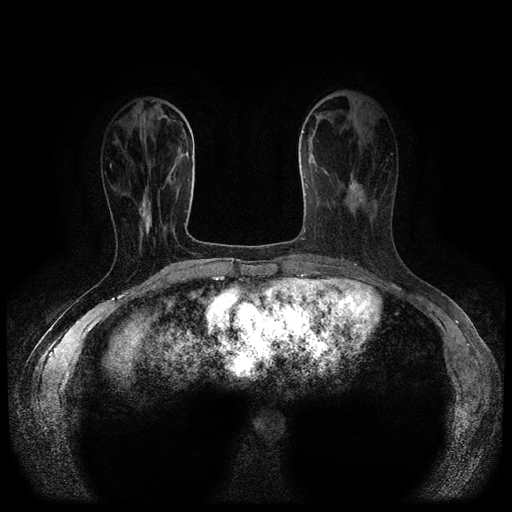
Breast MRI (dynamic contrast-enhanced, multi-phase), one axial slice; position 33 of 116 along the scan axis; dynamic contrast-enhanced series, time point 2 of 5 at this slice position (early post-contrast); 1.5 T; TE 2.6 ms, TR 5.4 ms; 2 mm slice thickness; 512 × 512 image matrix, field of view 340 × 340 mm. Patient: female, 47 years.
Annotated regions visible in this slice (semi-automatic segmentation, software-assisted and operator-edited):
- breast lesion (labelled 'tumour' in the annotation; benign lesions carry a separate 'benign' label): bounding box (x1, y1, x2, y2) in pixels: (347, 174, 364, 212)
- breast lesion (labelled 'tumour' in the annotation; benign lesions carry a separate 'benign' label): (138, 188, 152, 234)